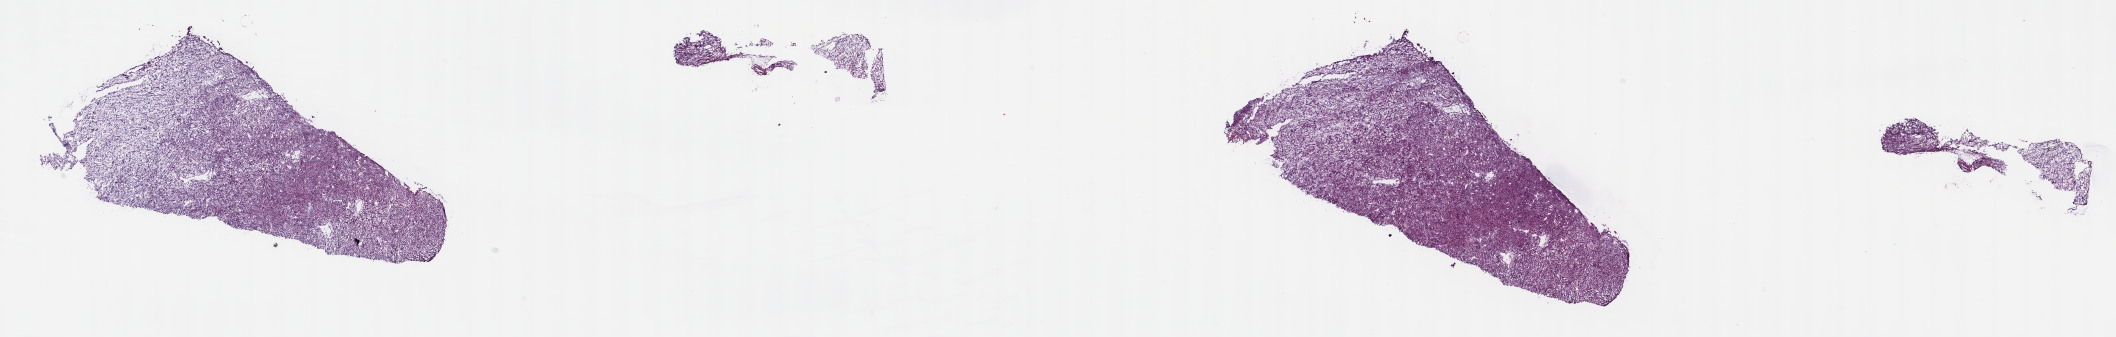
Hematoxylin and eosin (H&E) stained whole-slide image — low-resolution overview of the scanned area, about 34.2 x 5.5 mm (slide scanned at 40x); frozen section; primary tumour sample from the retroperitoneum and peritoneum. Patient: male, age at initial diagnosis 67 years. Slide review estimates, as recorded: tumour cells 100%, tumour nuclei 80%, normal cells 0%, stromal cells 0%, necrosis 0%. Inflammatory infiltration, as recorded: lymphocyte infiltration 2%, monocyte infiltration 0%, neutrophil infiltration 0%.
Pathologic diagnosis: Dedifferentiated liposarcoma.